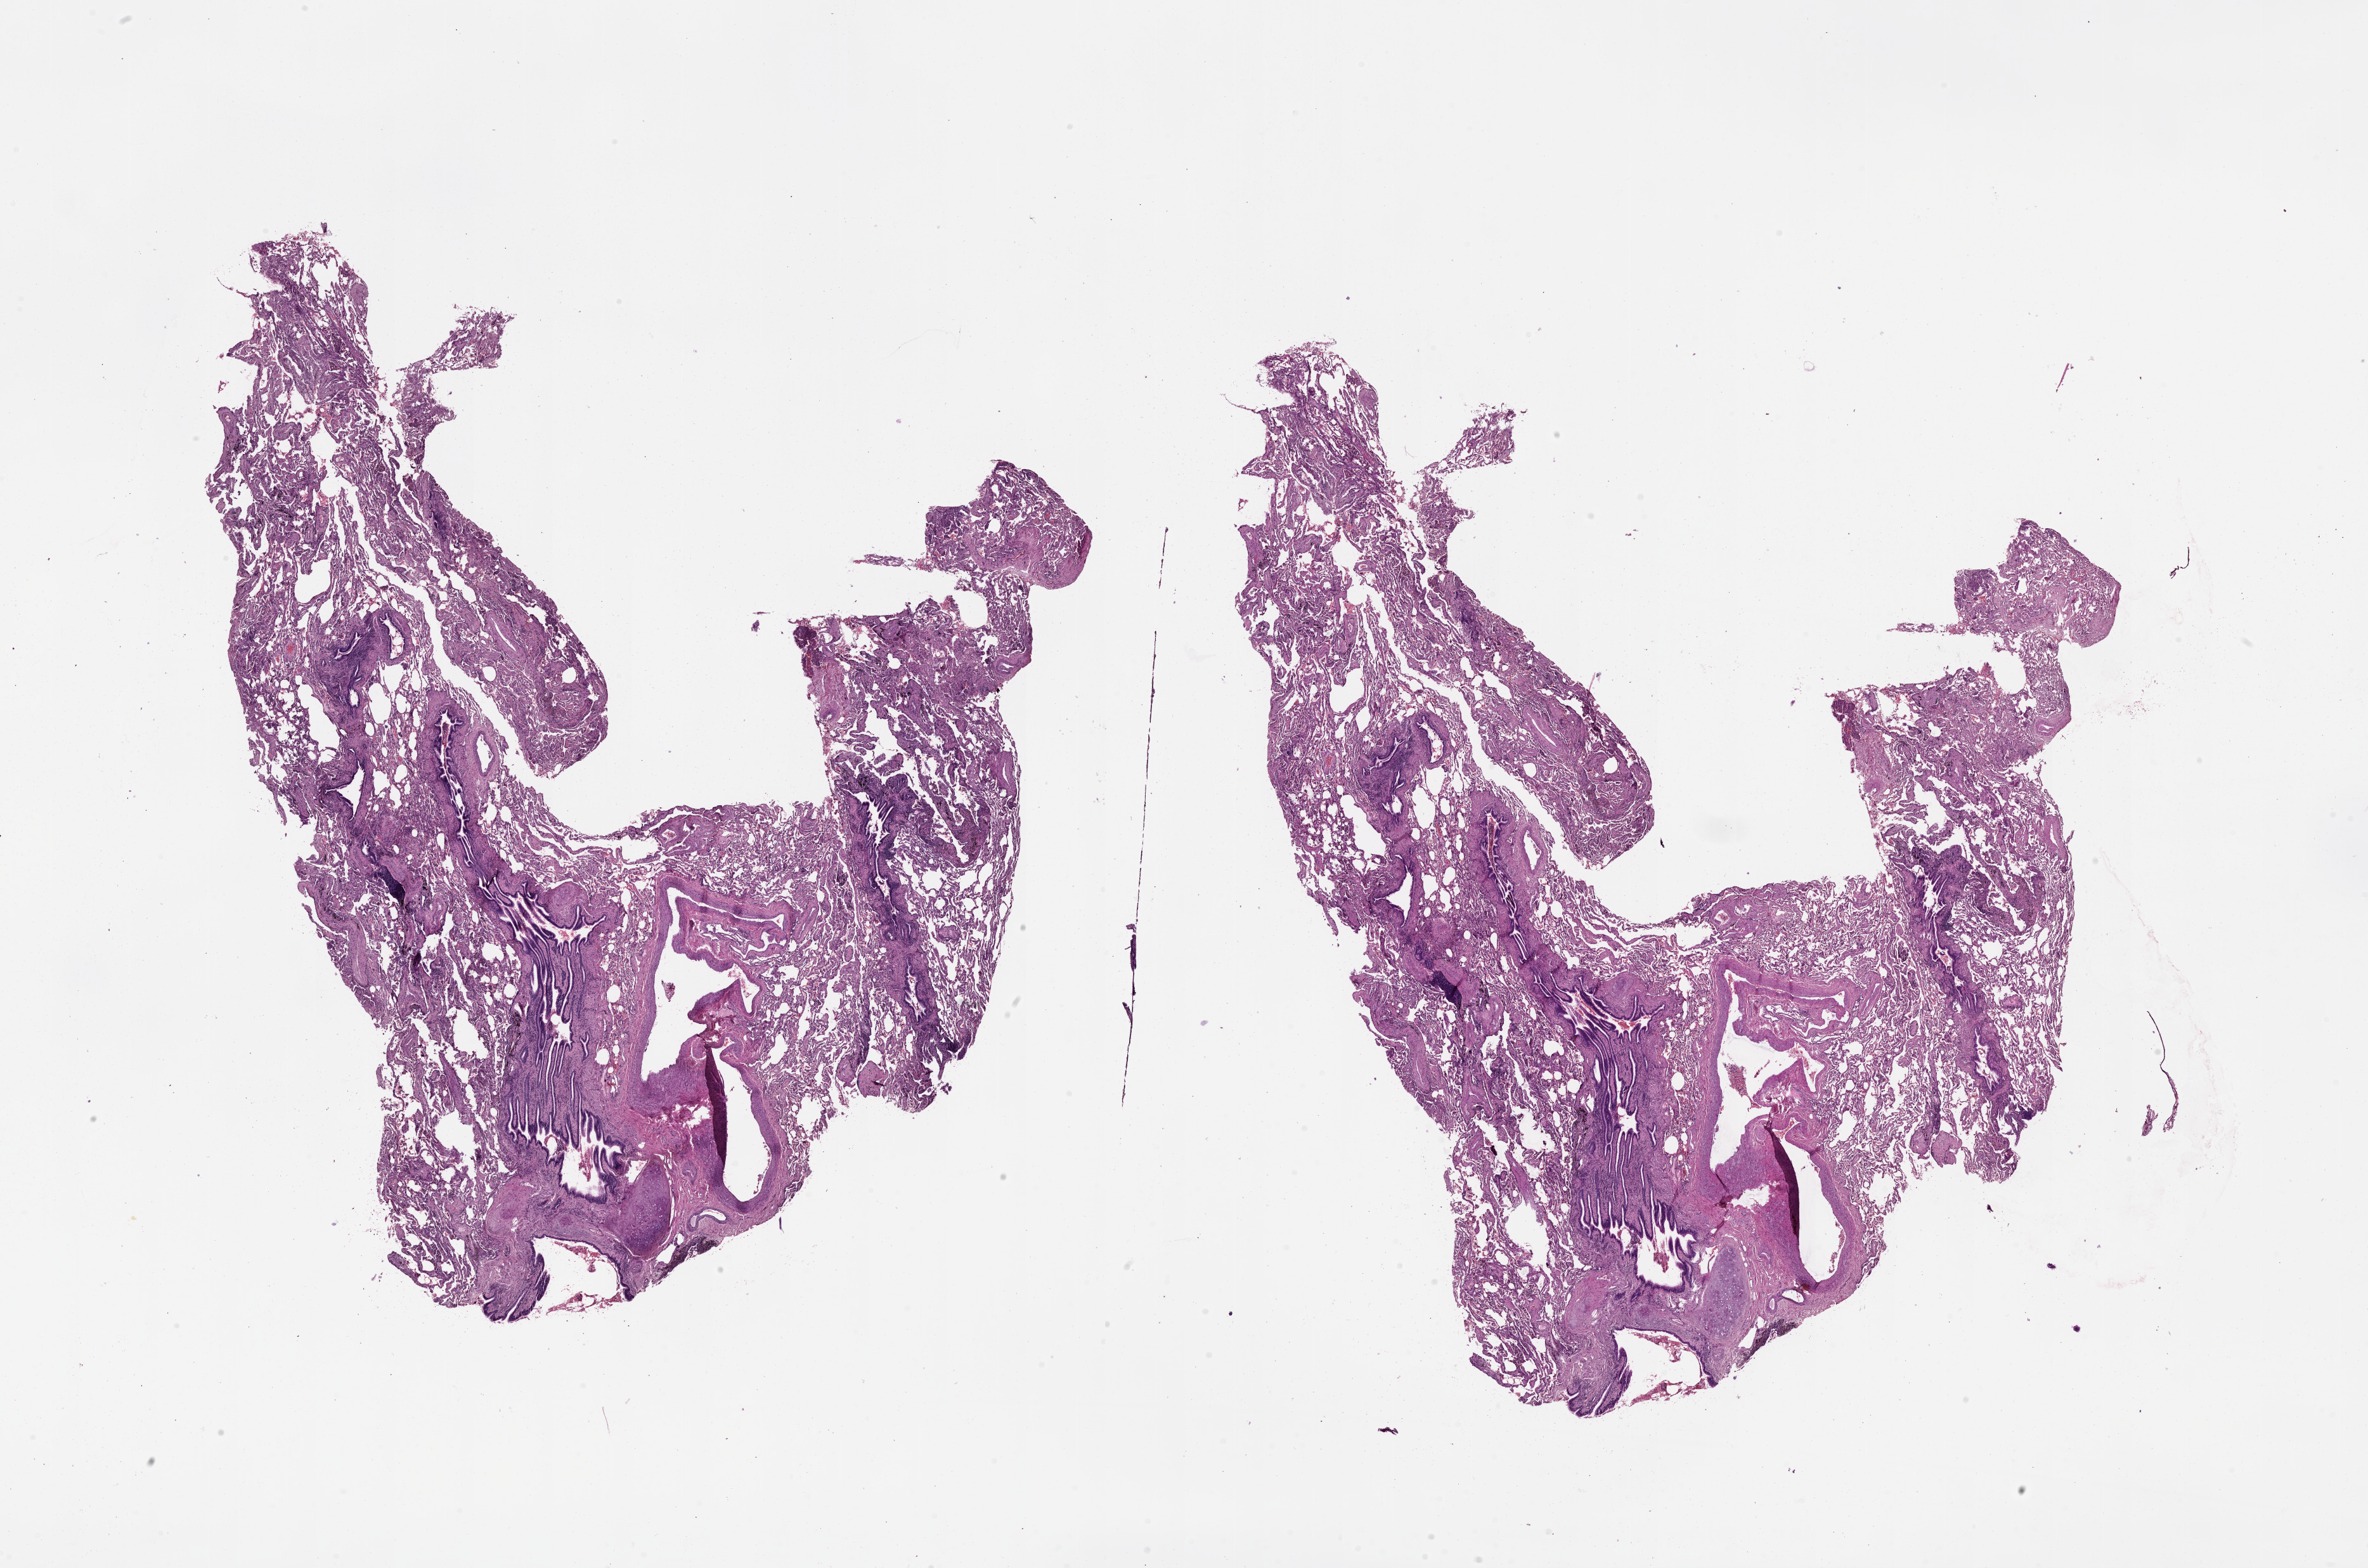
Whole-slide histology image, H&E-stained, whole scanned area (about 30.1 x 19.9 mm) shown as a low-resolution overview. Lung, normal (non-tumour) tissue. Male, 66 y/o.
- this section: normal (non-tumour) tissue from the same patient
- patient diagnosis (cohort enrolment): squamous cell carcinoma (lung)